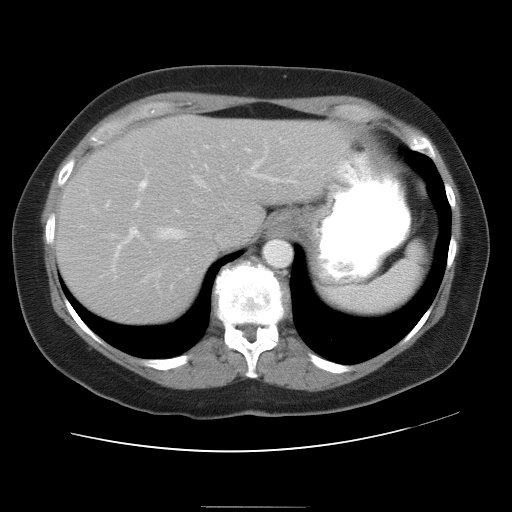
Contrast-enhanced abdominal CT, one axial slice. Slice 25 of 30 in the series (ordered by position). Reconstruction kernel STANDARD. 120 kVp. Intravenous contrast given. Soft-tissue window (W 400 / L 40 HU). 7.5 mm slice thickness. 512 × 512 image matrix, field of view 376 × 376 mm. Female patient, age 52 years. Case-level facts recorded for this patient, not image findings: diagnosis: colorectal cancer liver metastases, imaged before liver resection; multiple liver metastases: no; largest metastasis: 3 cm; disease in both lobes: yes.
Outlined on this slice (expert manual segmentation):
- hepatic veins: bounding box (x1, y1, x2, y2) in pixels: (158, 161, 262, 239)
- liver: (55, 116, 336, 326)
- planned liver remnant (the part of the liver to remain after resection): (155, 116, 336, 230)
- portal vein (with intrahepatic branches): (125, 146, 272, 242)